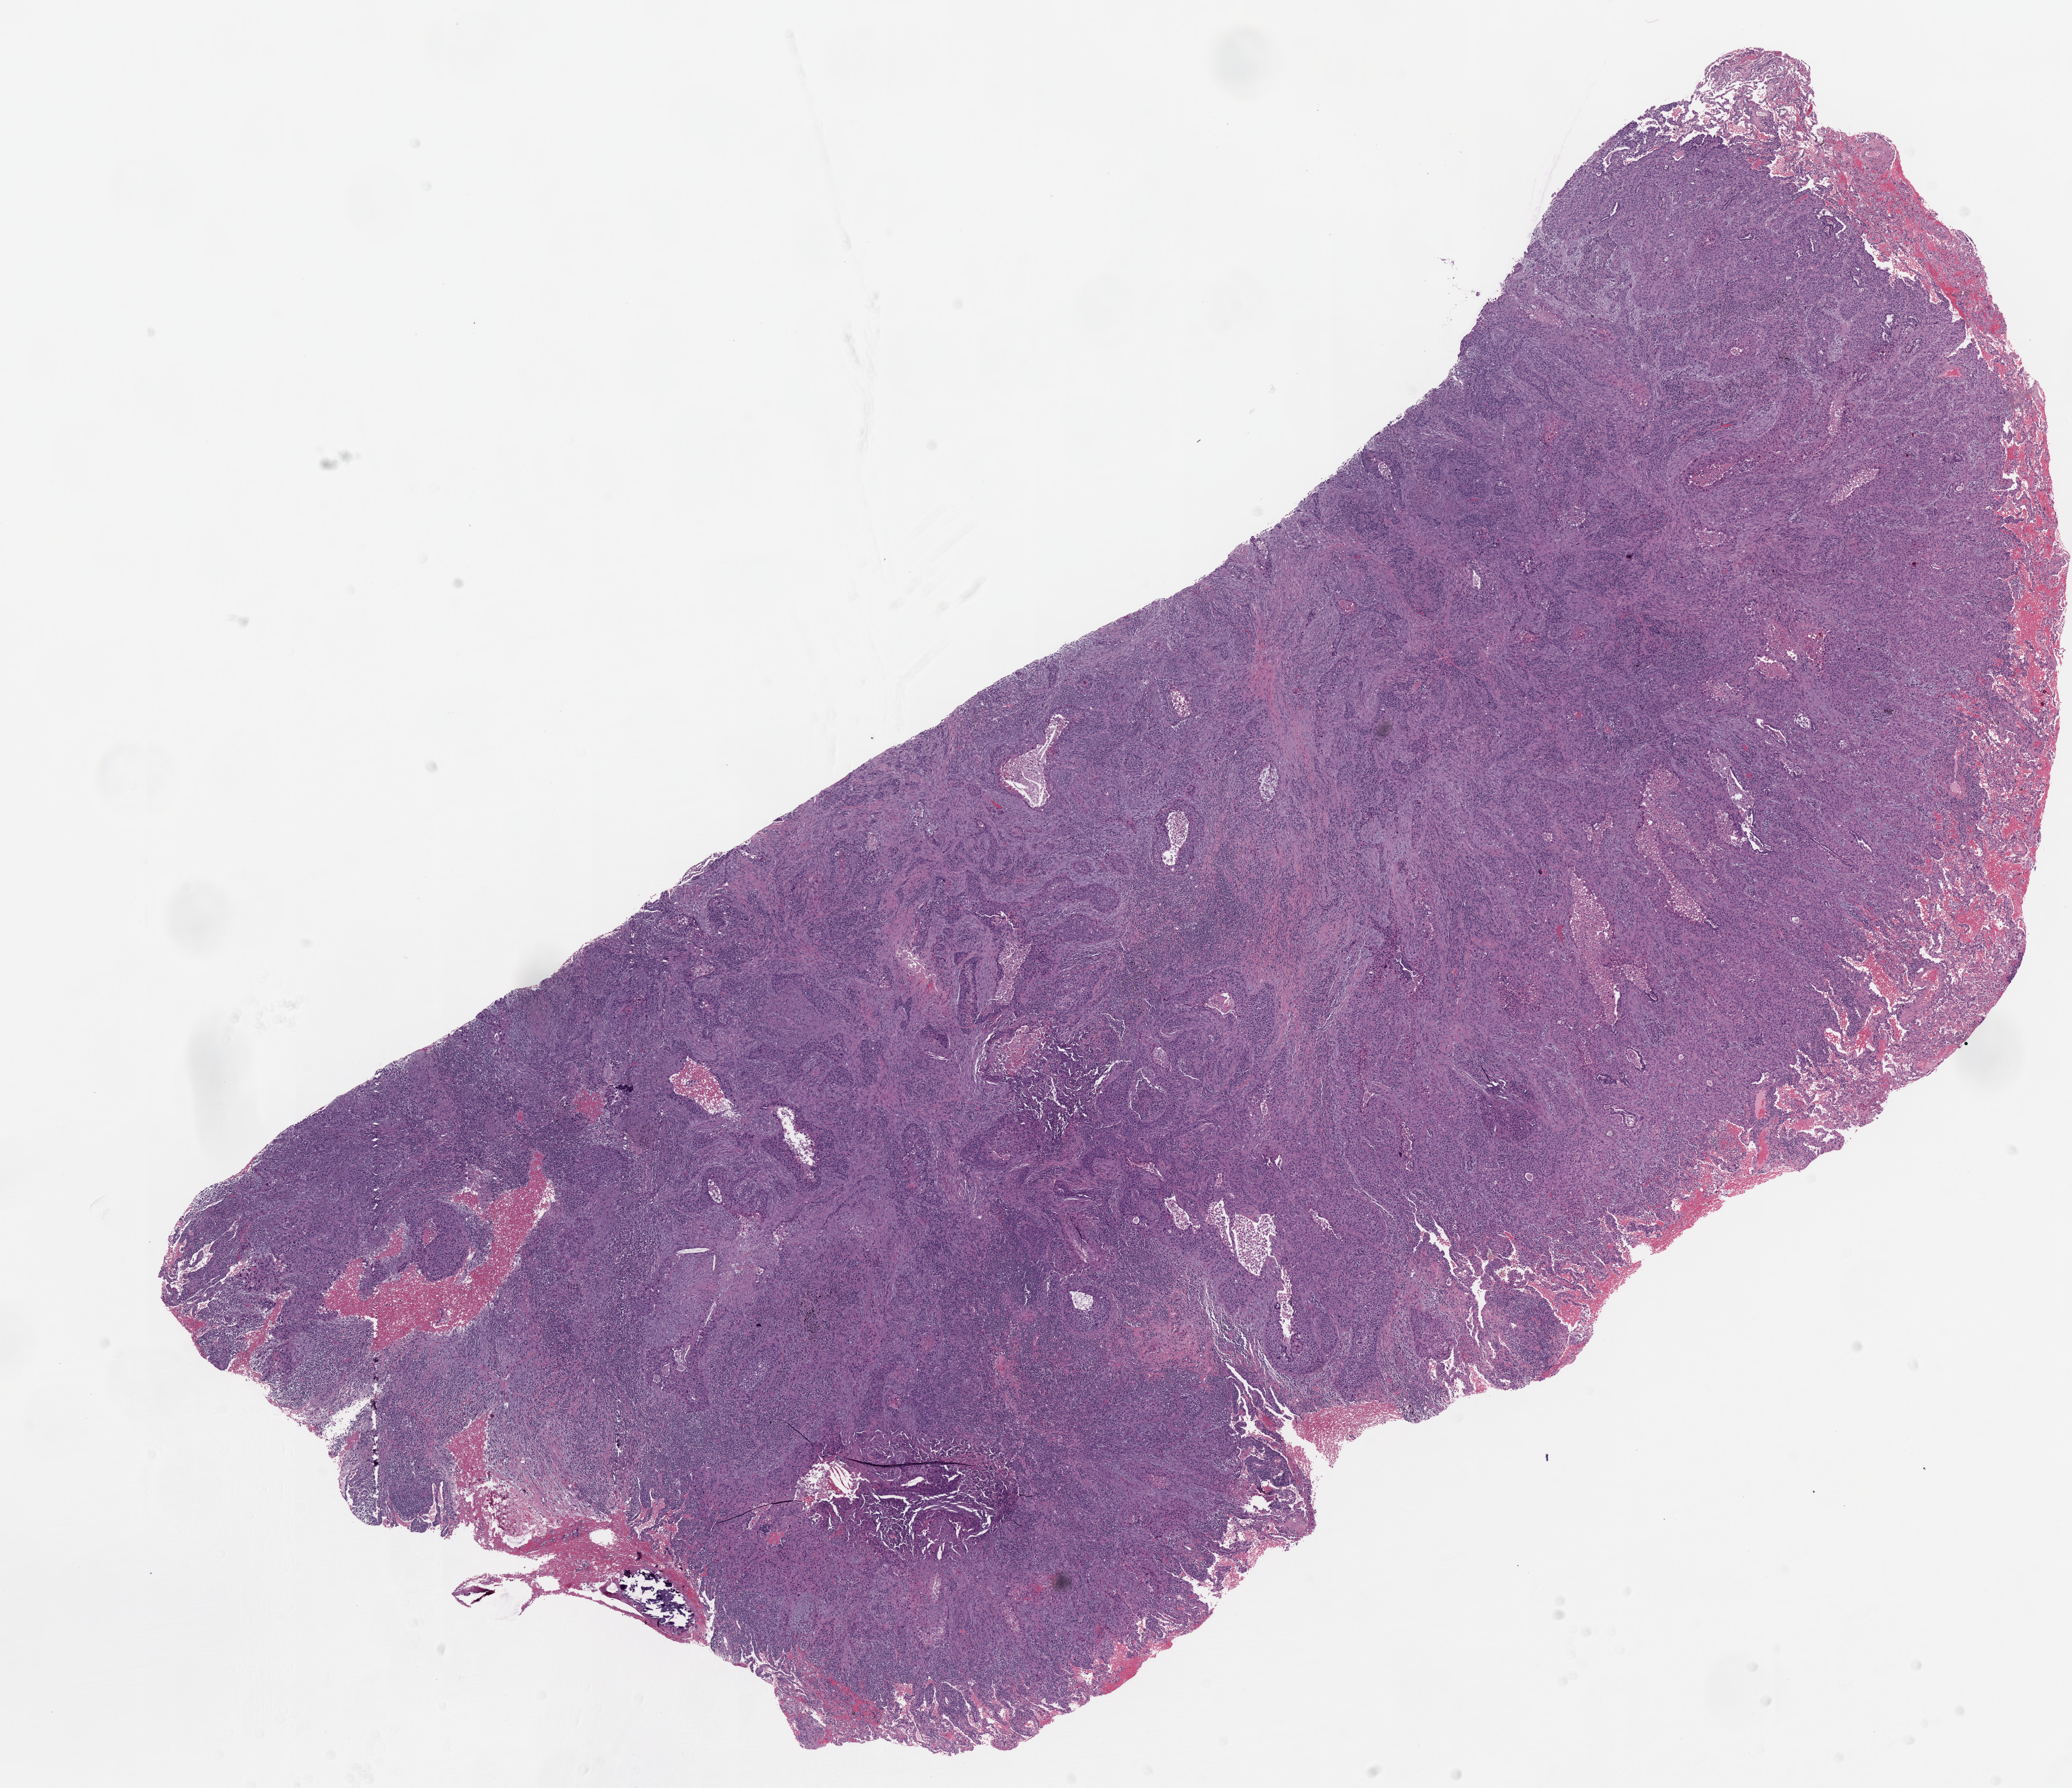
H&E-stained whole-slide image, shown as a low-resolution overview of the whole scanned area (about 14.0 x 12.1 mm, slide scanned at 20x). Formalin-fixed paraffin-embedded (FFPE) diagnostic section. Lung, primary tumour sample. Male patient; age at initial diagnosis 78 years.
- histologic diagnosis: Squamous cell carcinoma, NOS (upper lobe, lung)
- AJCC pathologic stage: IB (6th edition)